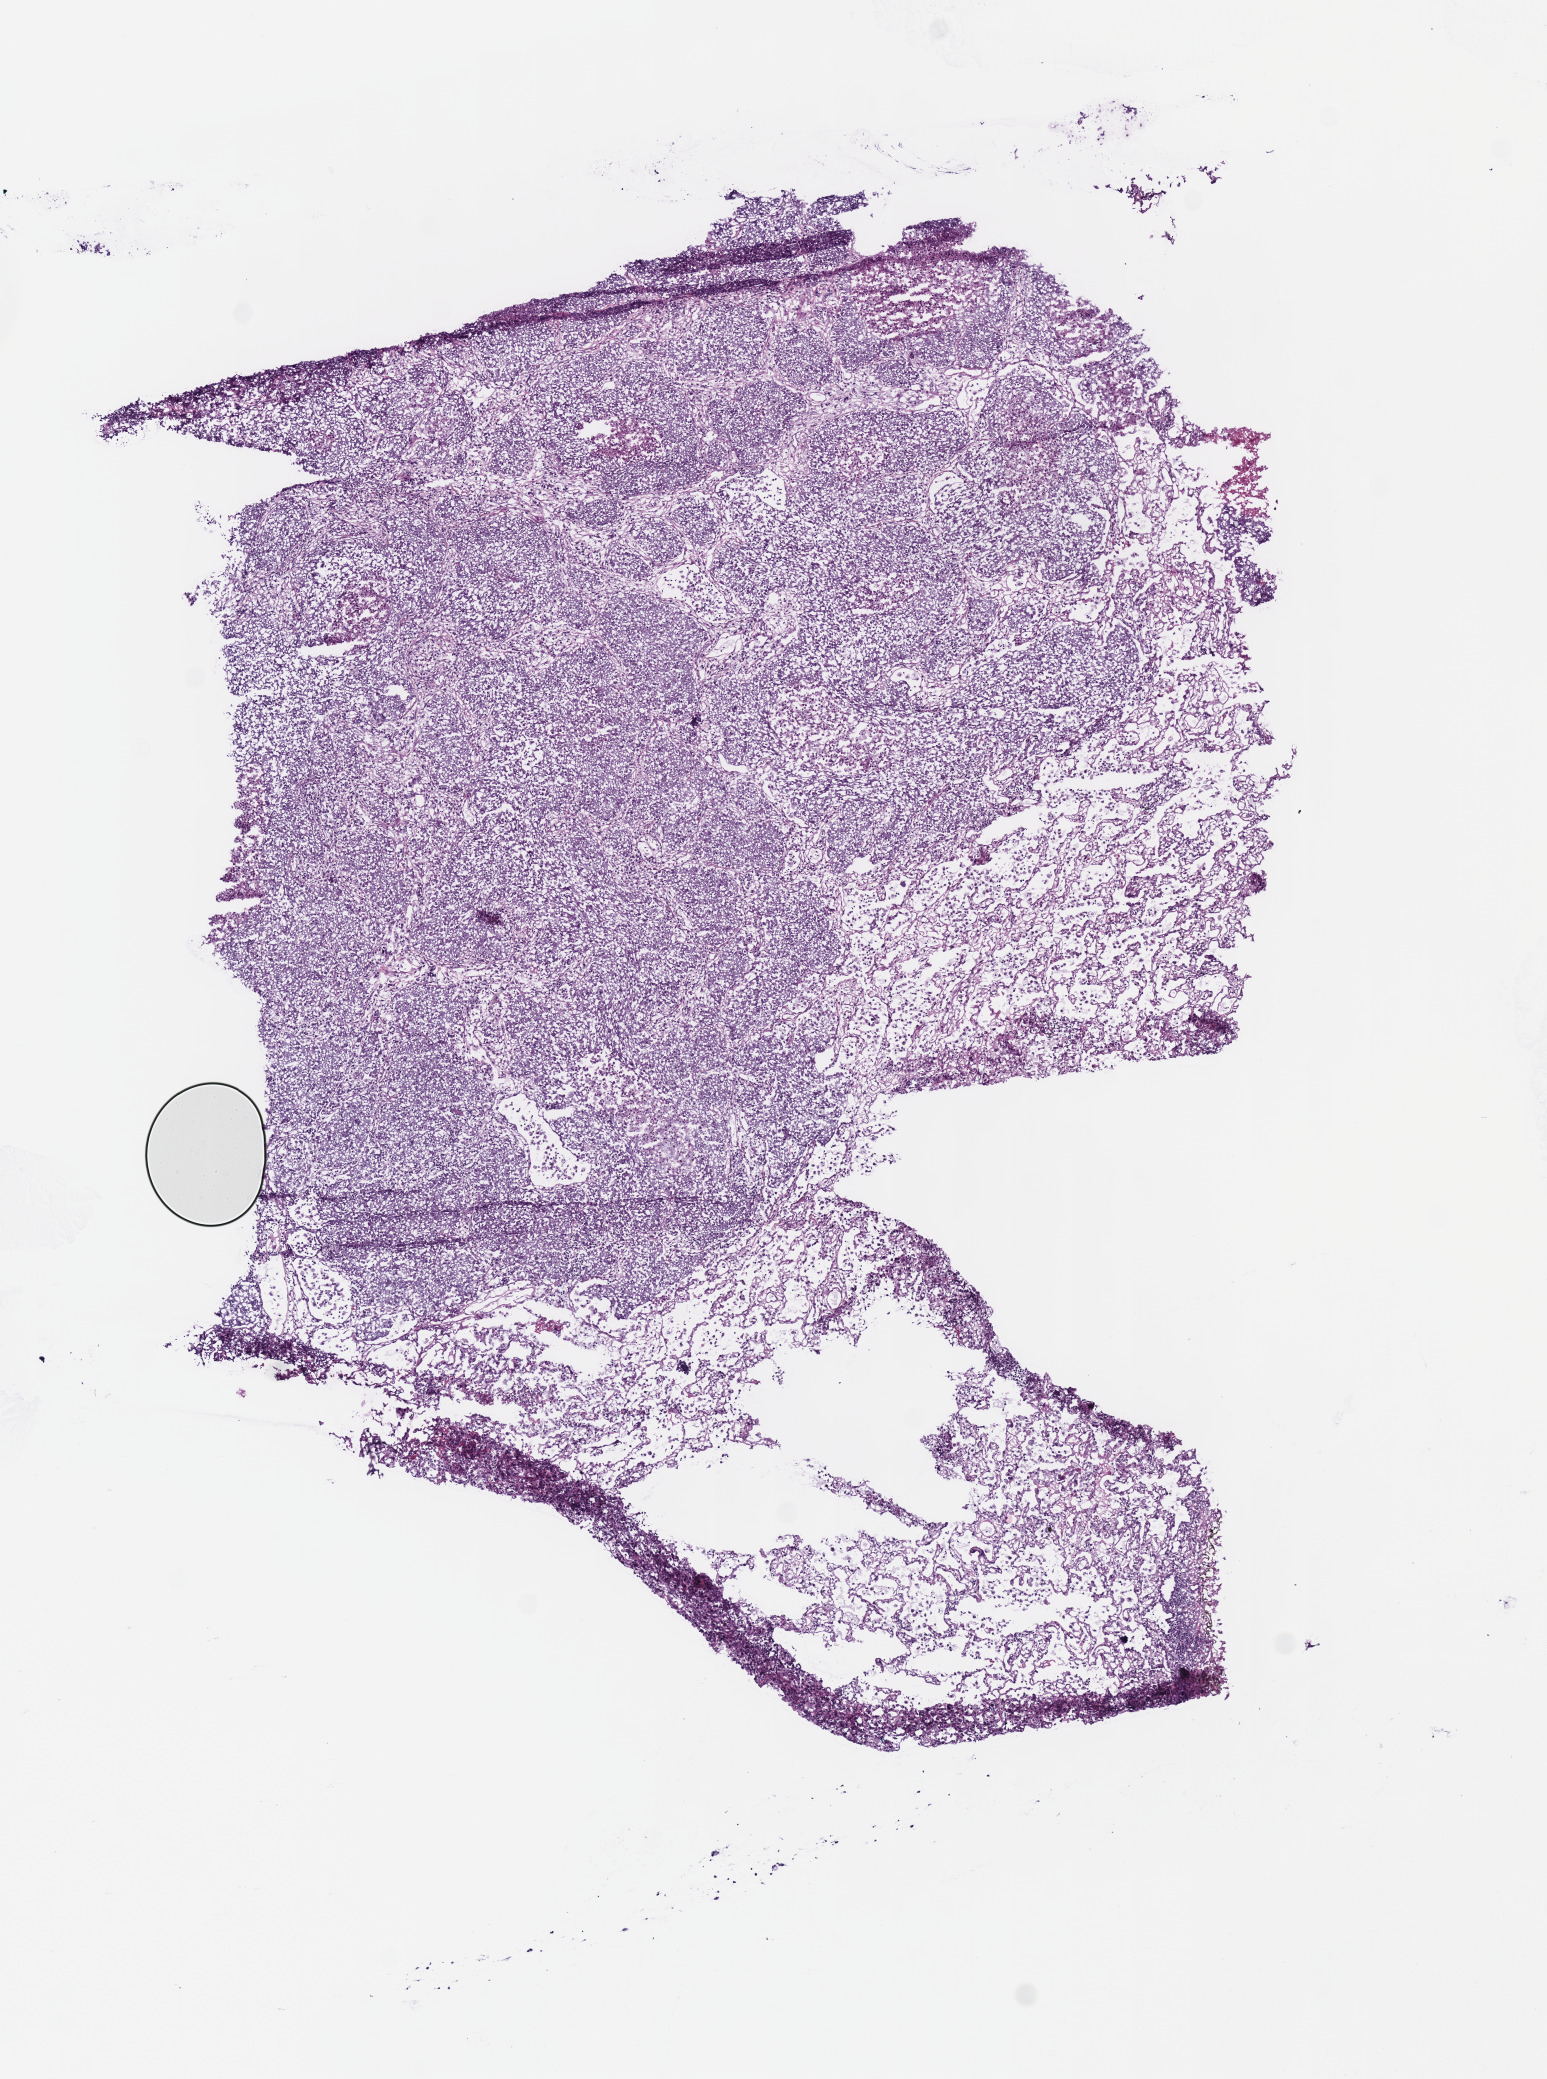
Hematoxylin and eosin (H&E) stained whole-slide image, a low-resolution overview of the entire scanned area, about 6.1 x 8.2 mm; frozen section from the top of the tissue portion; sample: primary tumour, lung. Male patient; age at initial diagnosis 68 years. Slide review estimates, as recorded: tumour cells 85%, tumour nuclei 70%, normal cells 14%, stromal cells 0%, necrosis 1%. Infiltration values recorded for this section: lymphocyte infiltration 15%, monocyte infiltration 5%, neutrophil infiltration 2%.
Histologic diagnosis: Squamous cell carcinoma, NOS.